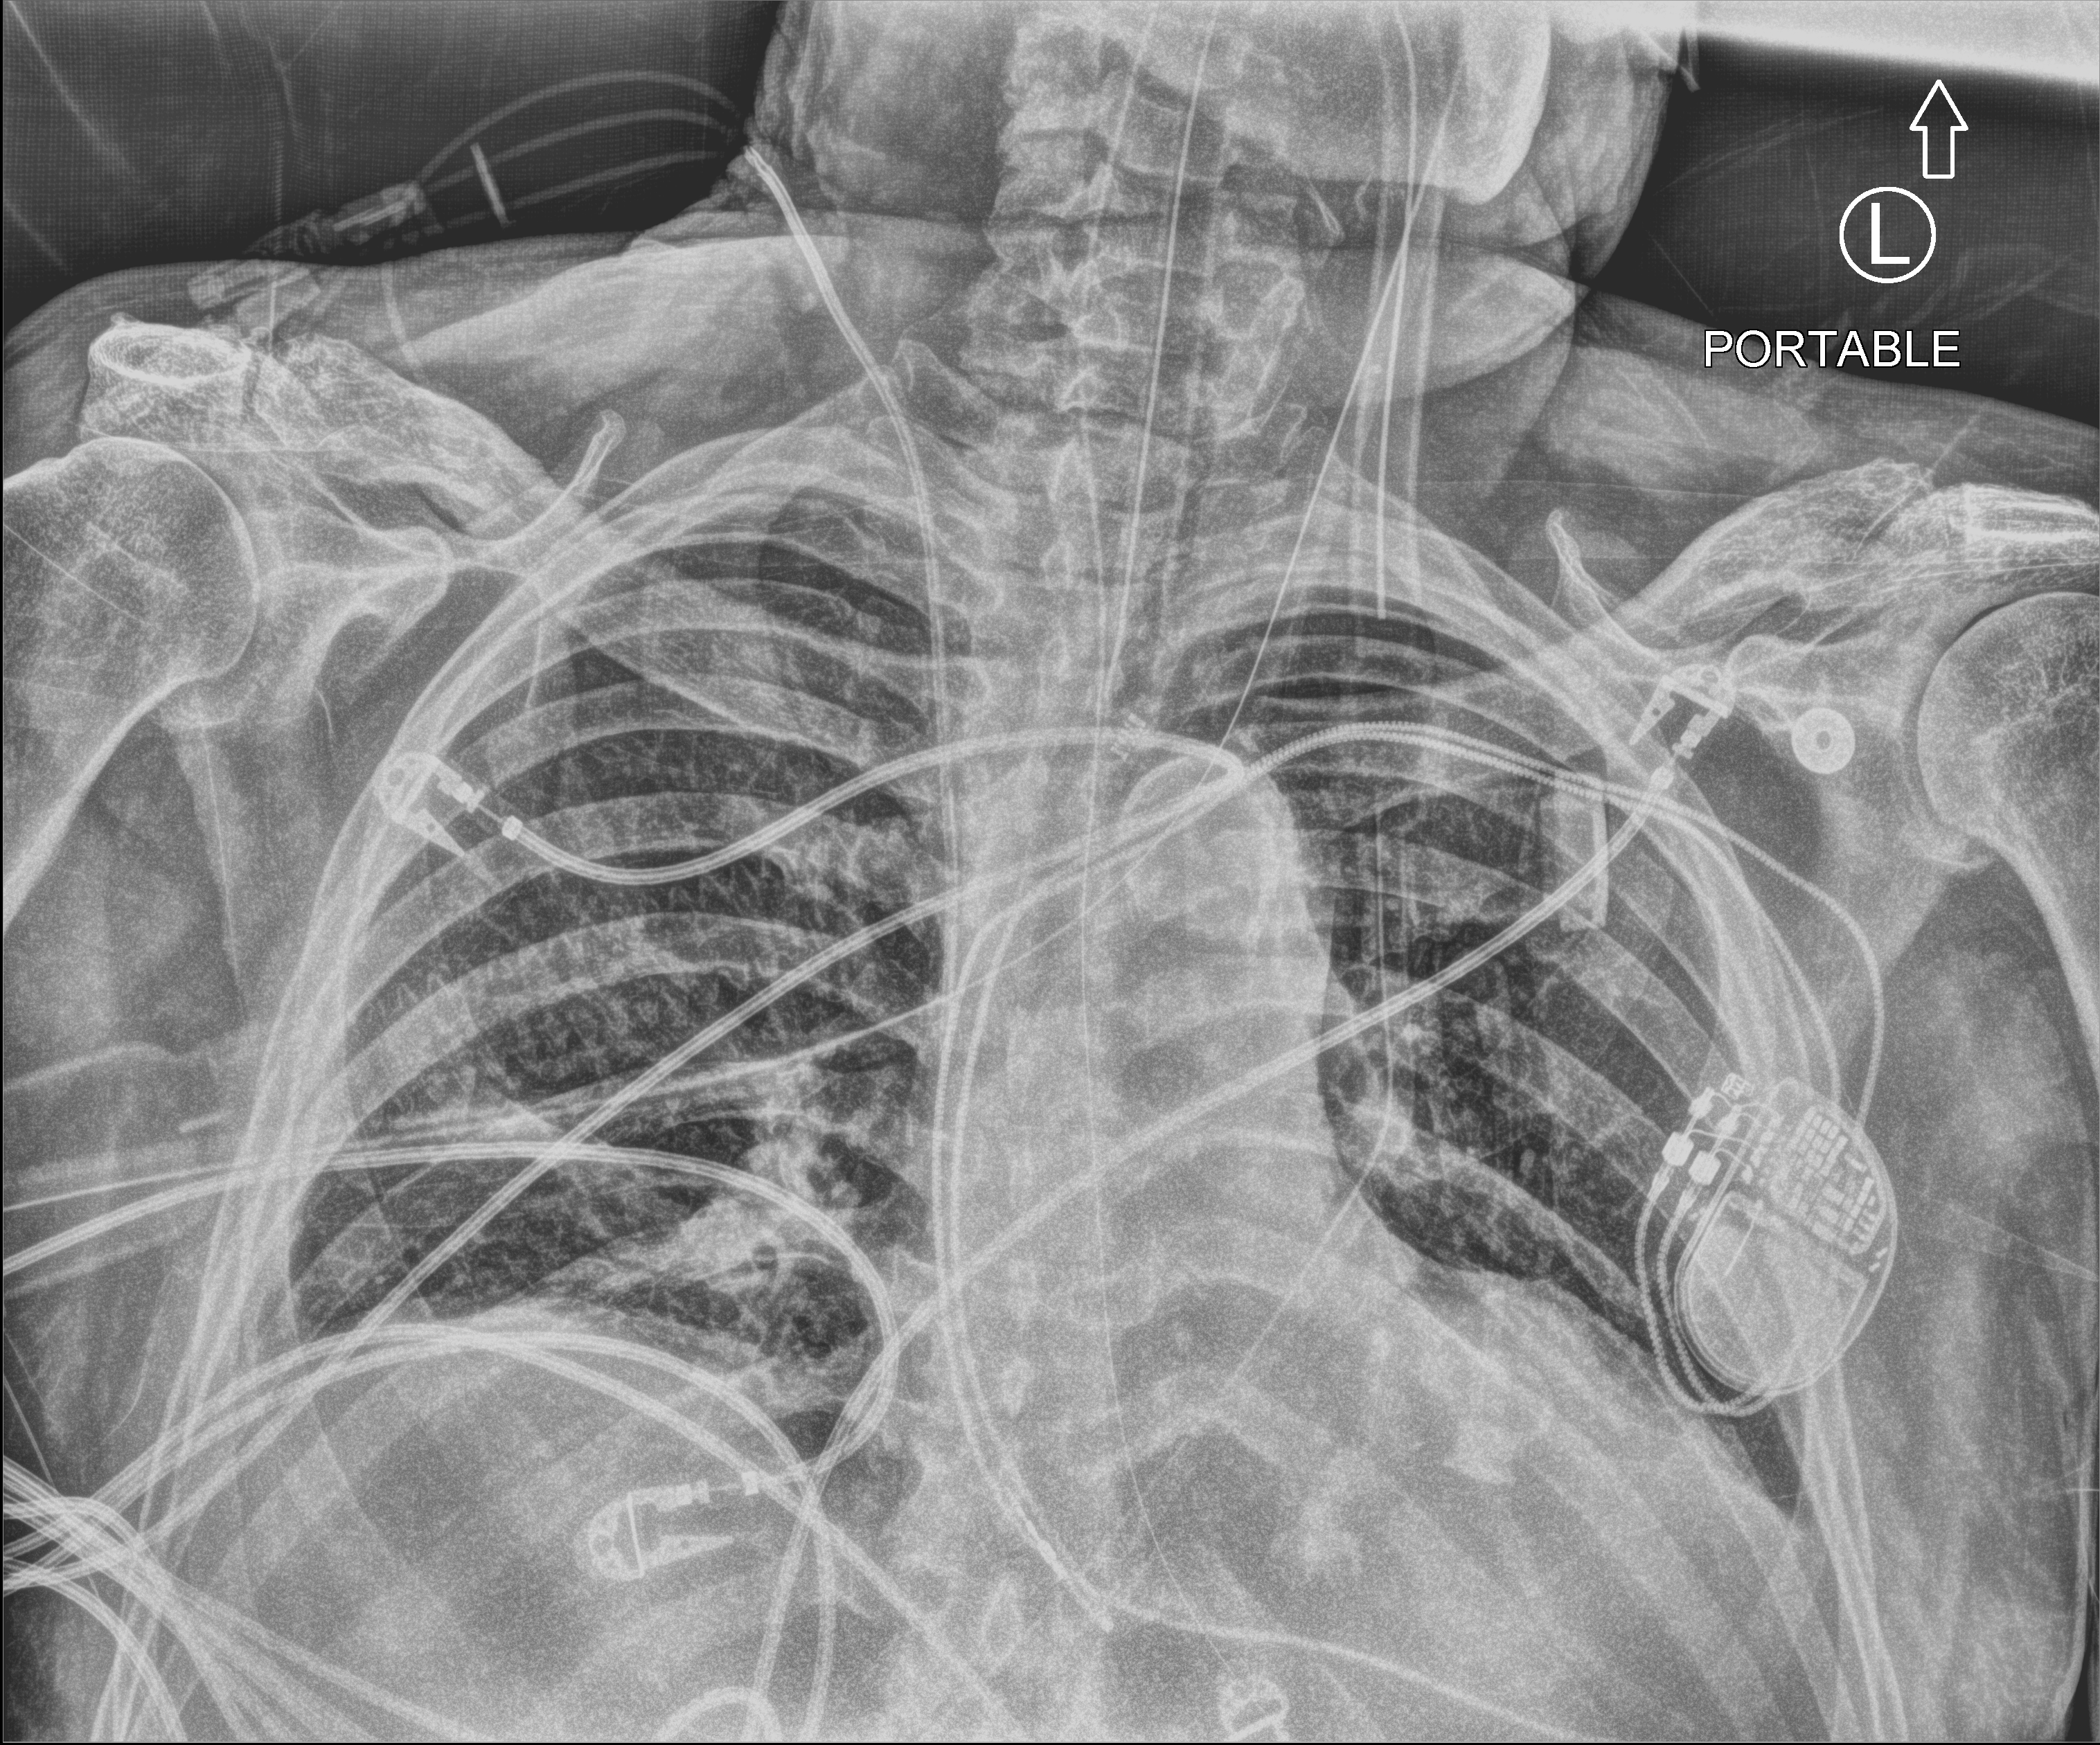
Portable chest radiograph; anteroposterior (AP) projection. Patient hospitalised with COVID-19; male, aged 60–74 years.
From the hospital-stay record, not from the radiograph (when in the stay this image was taken is not recorded):
- length of hospital stay: 41 days
- admitted to intensive care during this hospital stay: yes